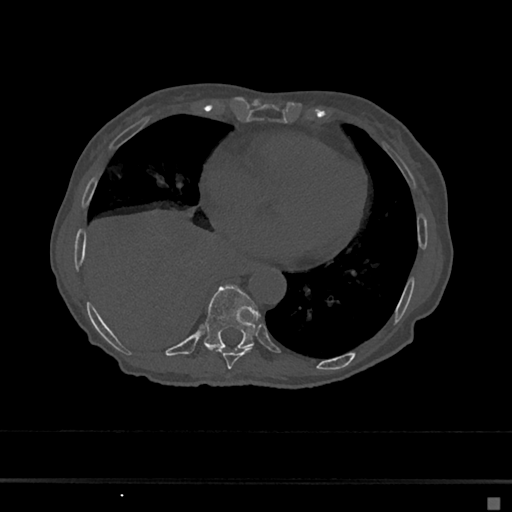
CT including the spine, one axial slice. Slice 295 of 797 in the series (ordered by position). Reconstruction kernel Br40s/3. Bone window (W 1800 / L 400 HU). 0.5 mm slice thickness. 512 × 512 image matrix, field of view 360 × 360 mm. Patient: female, 68 years. From the clinical record (not read from this slice): primary cancer: renal.
Structures marked on this image (semi-automatic segmentation, software-assisted and operator-edited):
- T8 vertebra: bounding box [x1, y1, x2, y2] px = [216, 347, 253, 369]
- T9 vertebra: [203, 285, 260, 350]